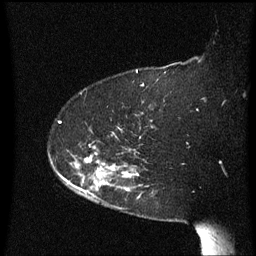
Breast MRI (dynamic contrast-enhanced), one sagittal slice. Slice 48 of 60 in the series (ordered by position). Dynamic contrast-enhanced series, image 2 of 3 at this slice position (ordered by acquisition). 1.5 T. TE 4.2 ms, TR 8.4 ms. 256 × 256 image matrix. Female patient, age 63 years. Case-level facts recorded for this patient, not image findings: setting: breast cancer imaged before/during neoadjuvant chemotherapy; receptor status: HER2-positive.
Outlined on this slice (semi-automatic segmentation, software-assisted and operator-edited):
- analysis volume of interest (the breast-tissue region the enhancement analysis was run in; not a lesion): bounding box <71,148,142,207> (left, top, right, bottom; pixels)
- tumour enhancement mask (voxels above the 70 % enhancement threshold inside the analysis volume of interest): <86,158,139,191>